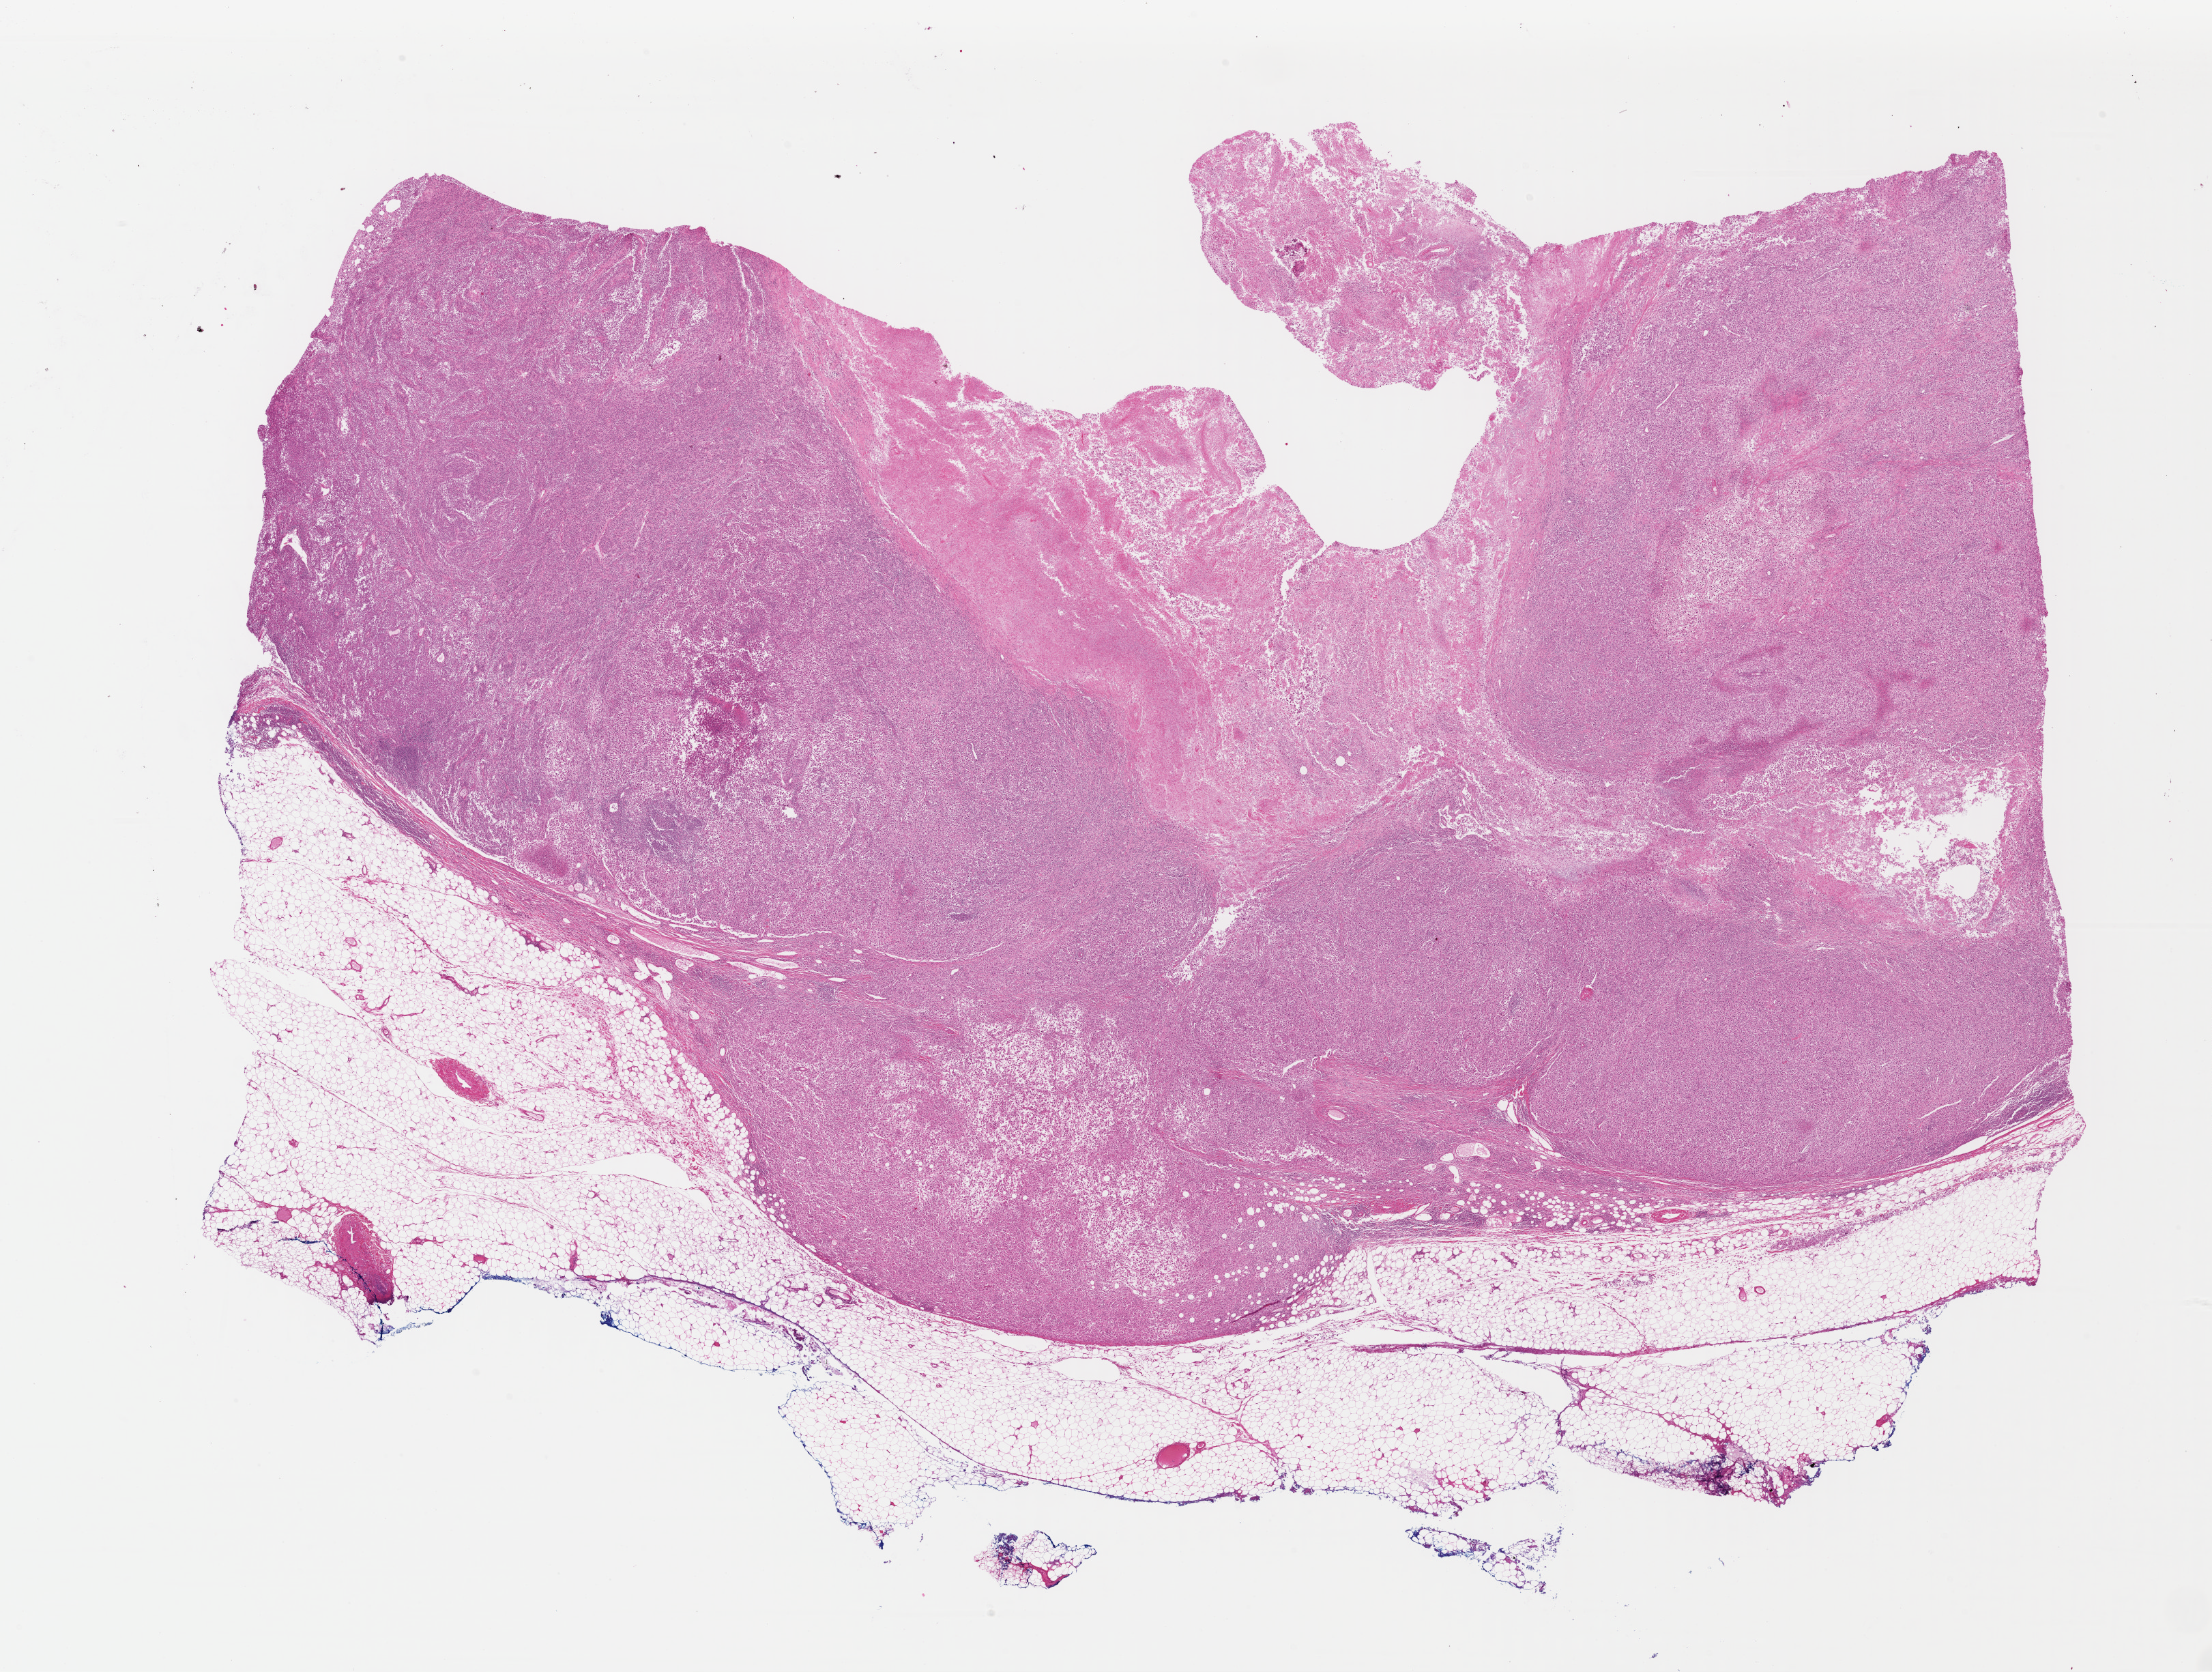
Hematoxylin and eosin (H&E) stained whole-slide image — low-resolution overview of the scanned area, about 25.5 x 19.3 mm (acquisition: 40x scan), formalin-fixed paraffin-embedded (FFPE) diagnostic section, skin, primary tumour sample. Male, age 73 years at initial diagnosis.
• pathologic diagnosis: Malignant melanoma, NOS